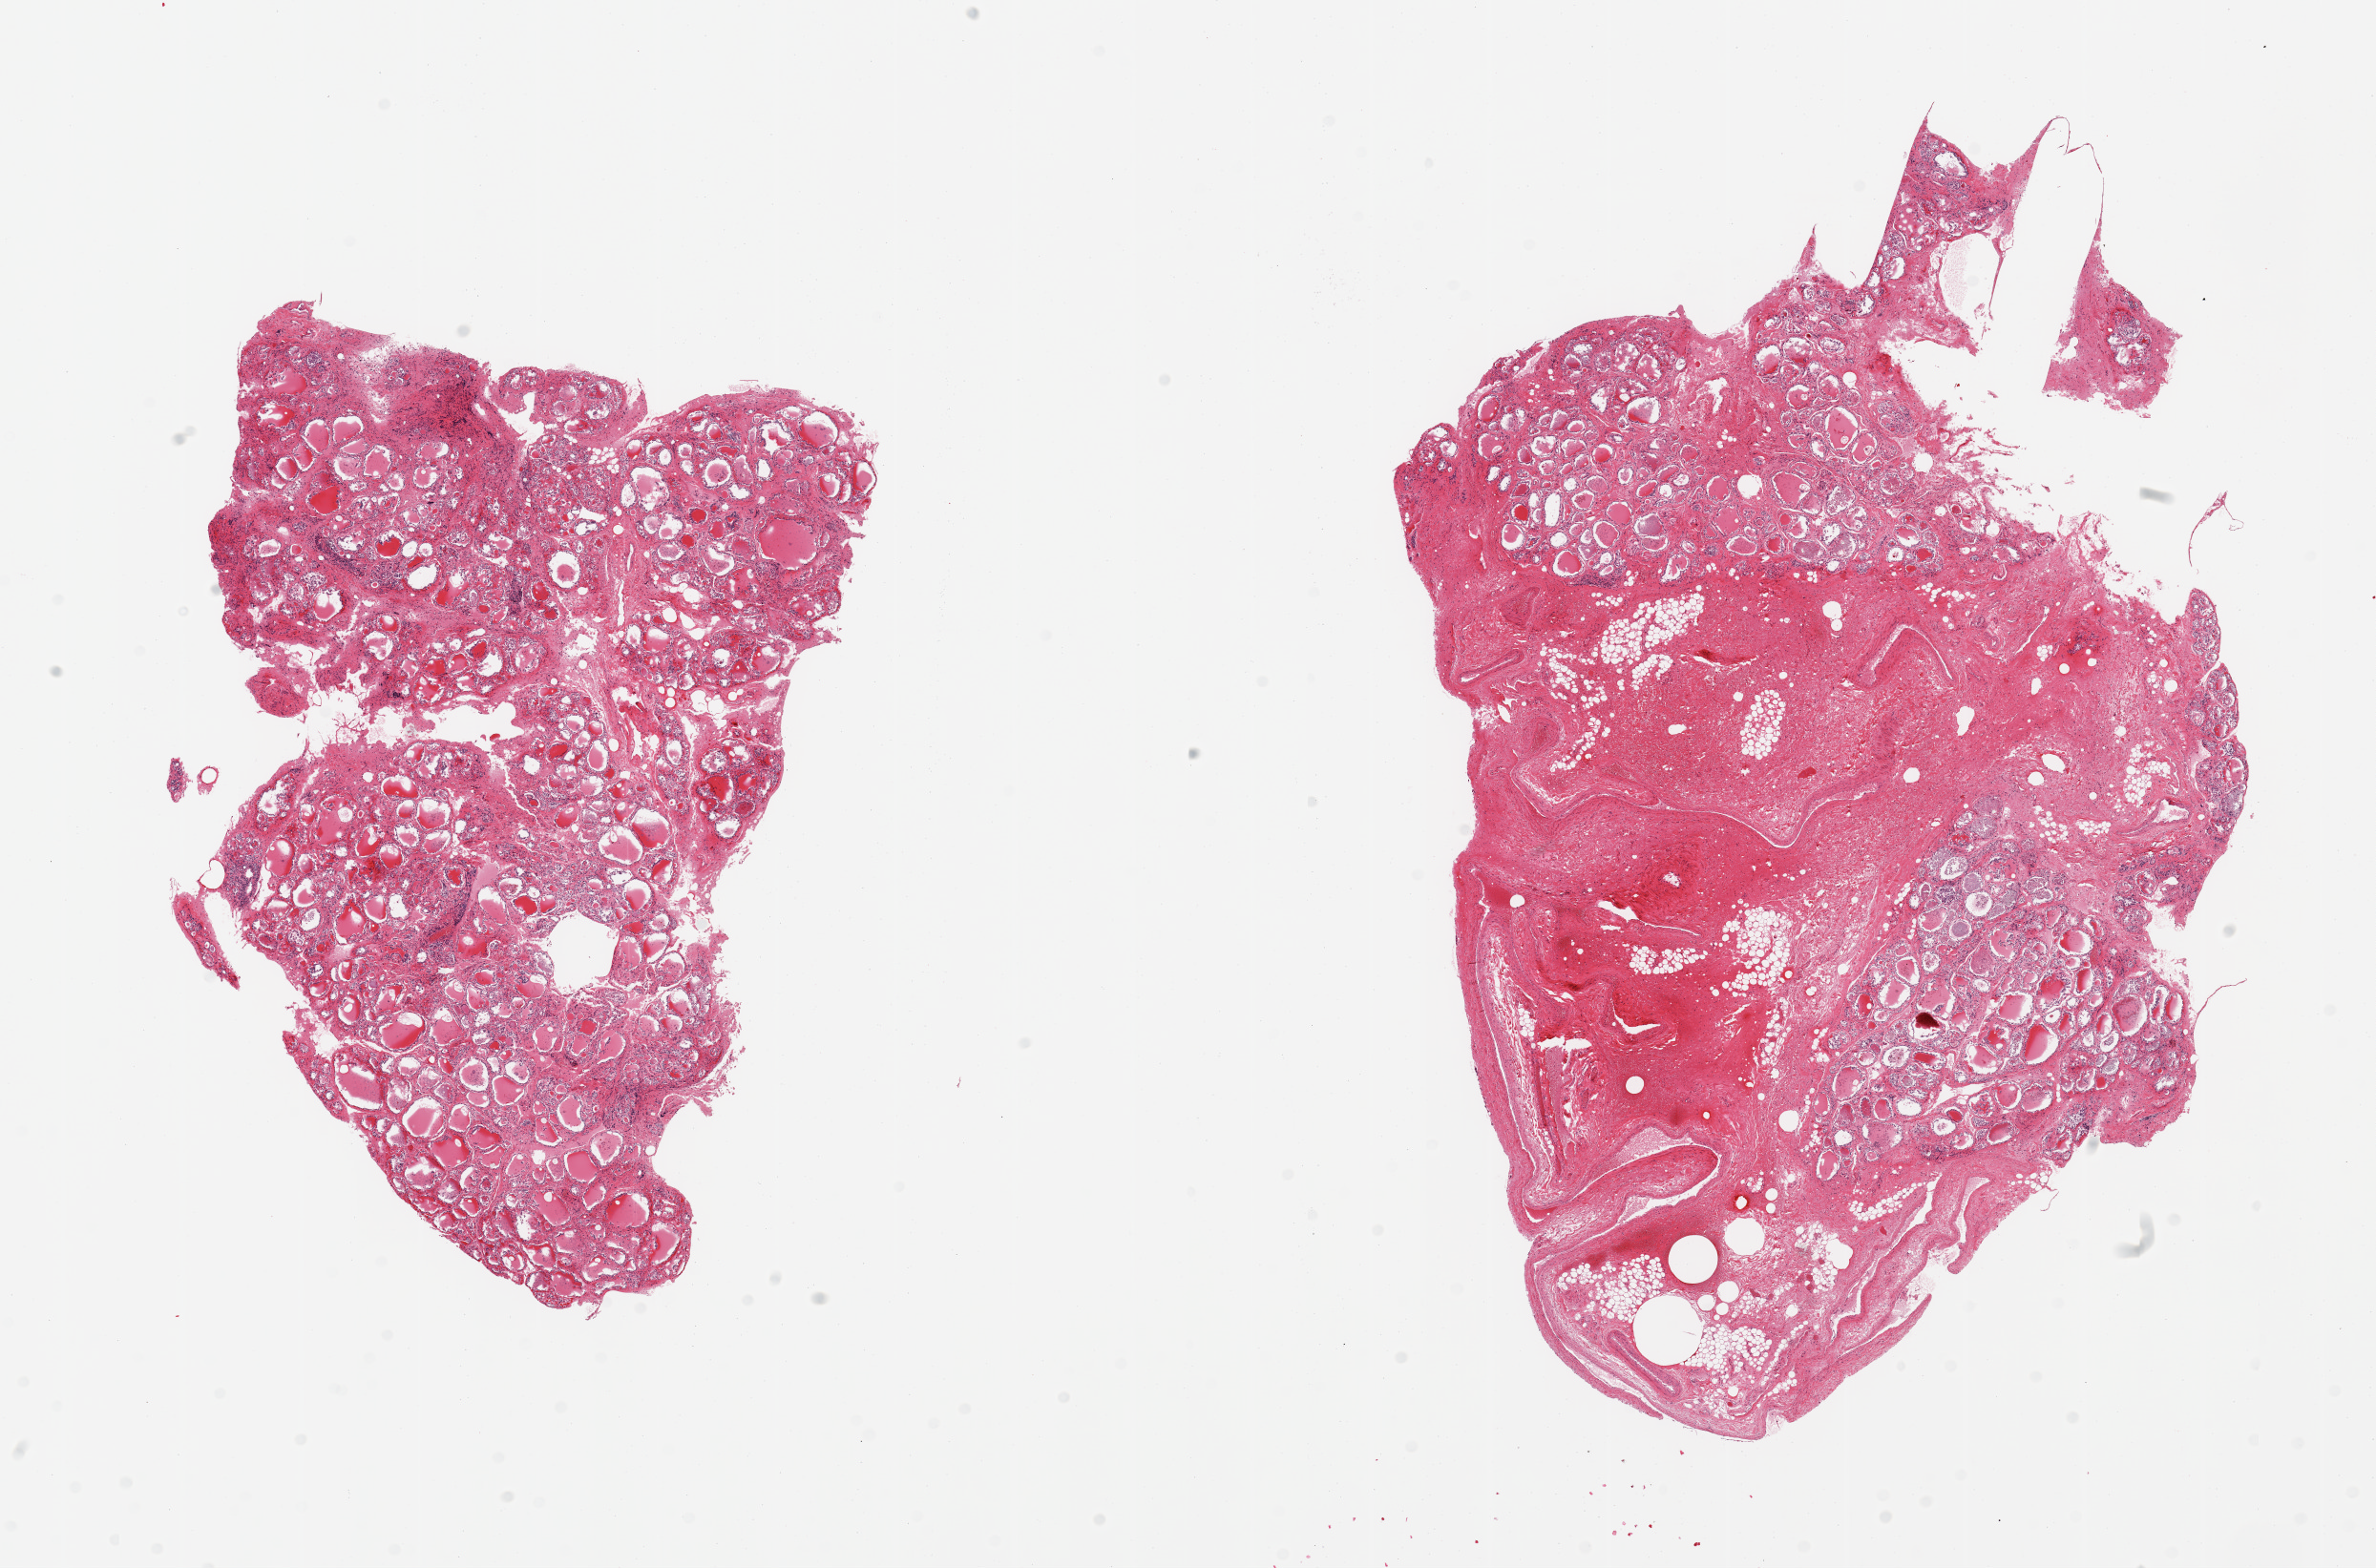
Digitized haematoxylin and eosin-stained section, brightfield, a low-resolution overview of the entire scanned area, about 19.7 x 13.0 mm. PAXgene-fixed, paraffin-embedded tissue. Target tissue: thyroid. Tissue donor sample. Donor sex: male.
Review note (as recorded): 2 pieces, ~30% adherent fibrous/fatty tissue (one aliquot).